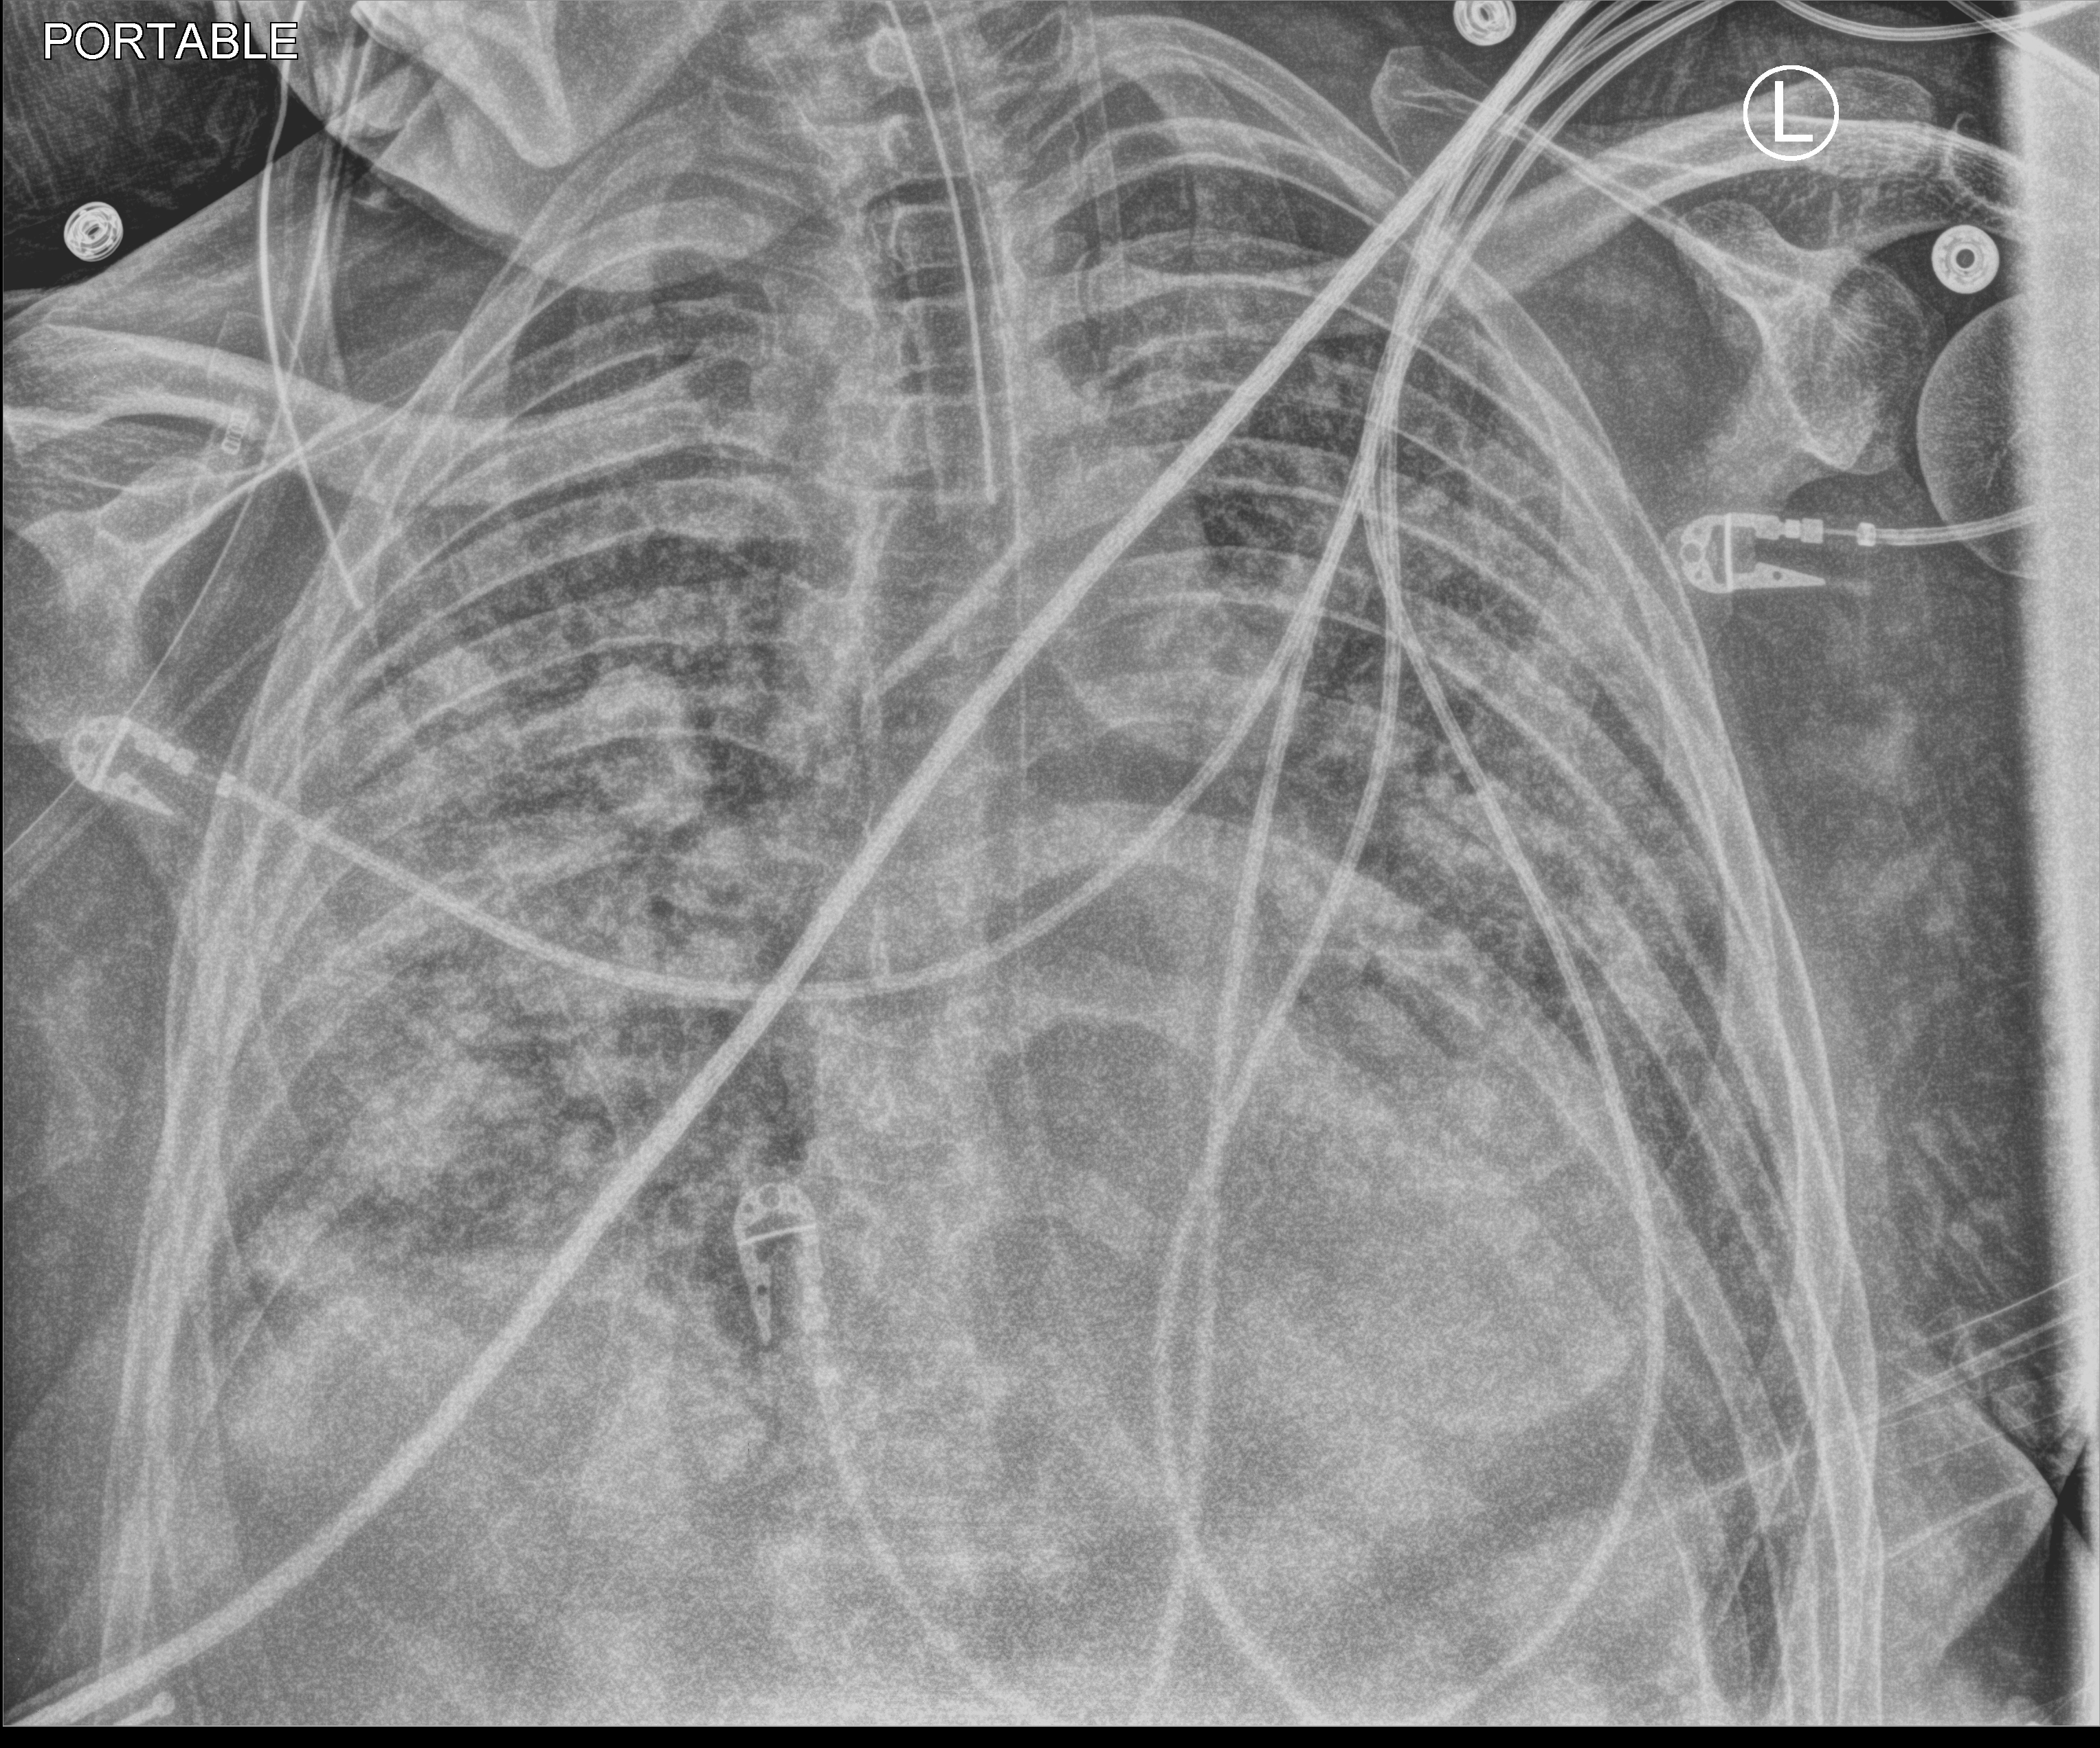
Chest X-ray (portable). Male patient hospitalised with COVID-19, age 18–59 years.
Hospital-stay facts (about this admission, not read from this image; timing relative to this image not recorded):
- COPD (admission record): no
- chronic kidney disease (admission record): no